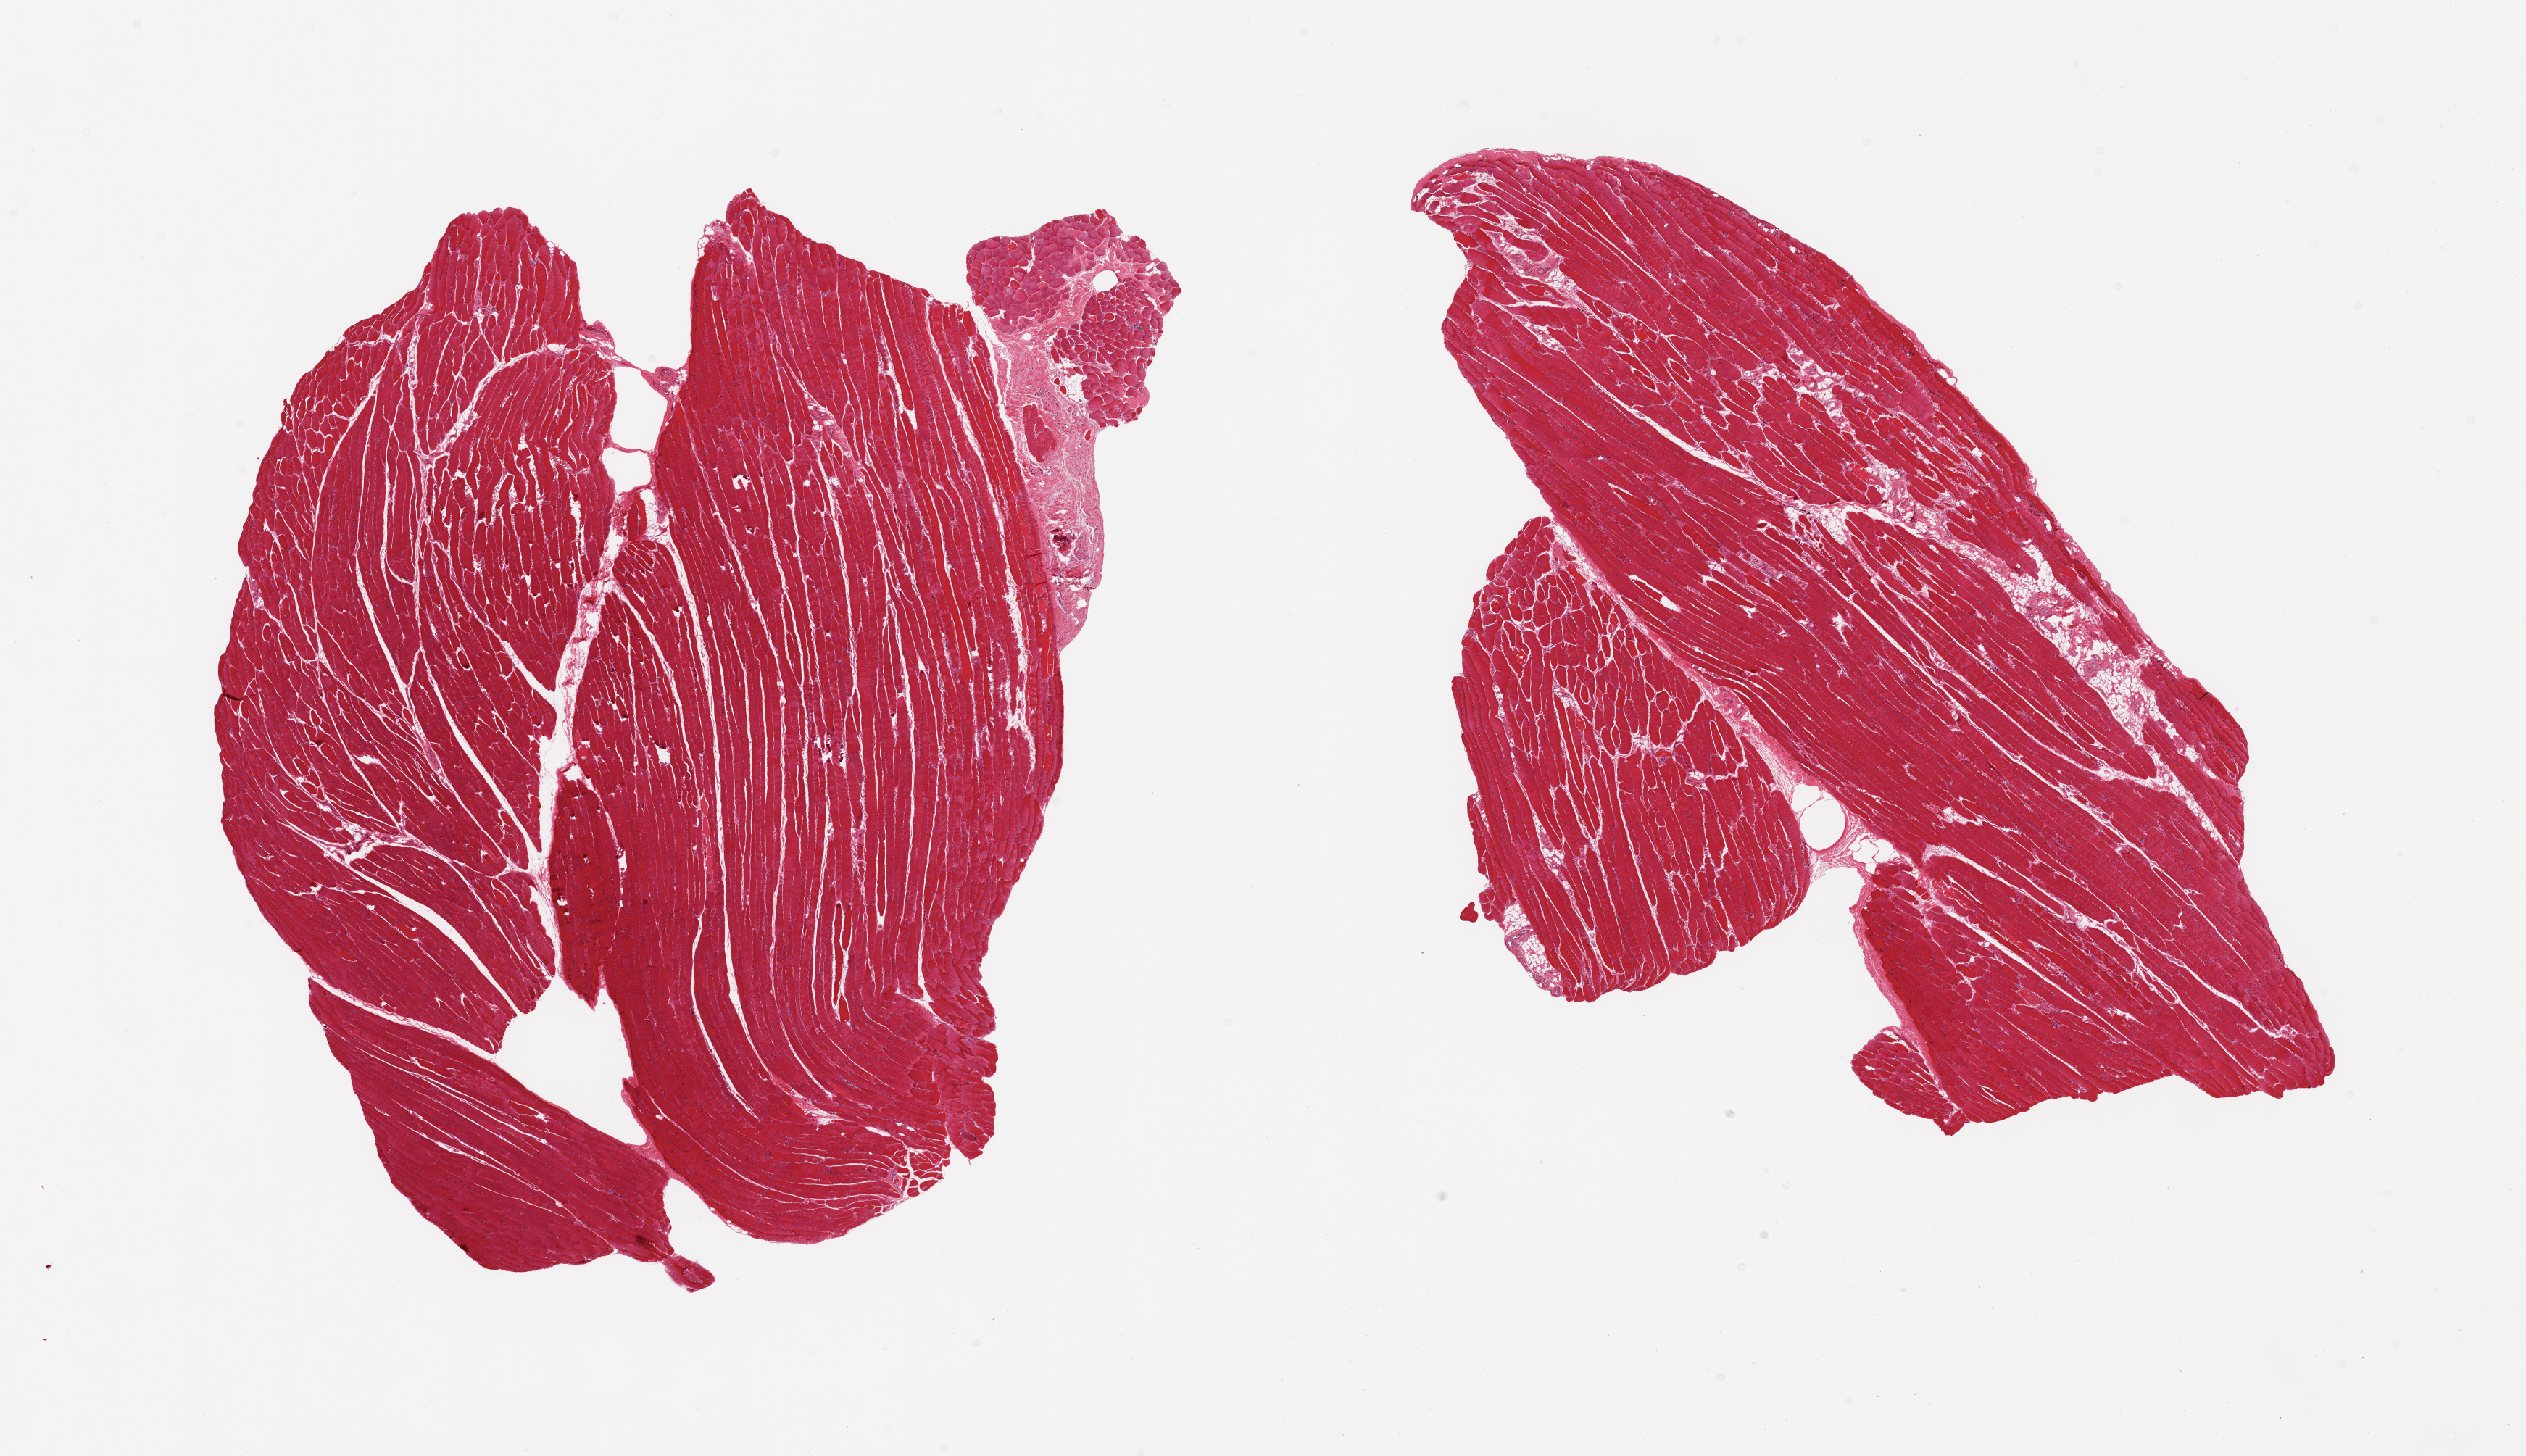
Digitized haematoxylin and eosin-stained section, a low-resolution overview of the entire scanned area, about 27.6 x 15.9 mm; PAXgene-fixed paraffin-embedded (PFPE) section; section of skeletal muscle (target tissue); donor tissue sample.
* review note (as recorded): 2 pieces, ~10% interstitial fat/fascia